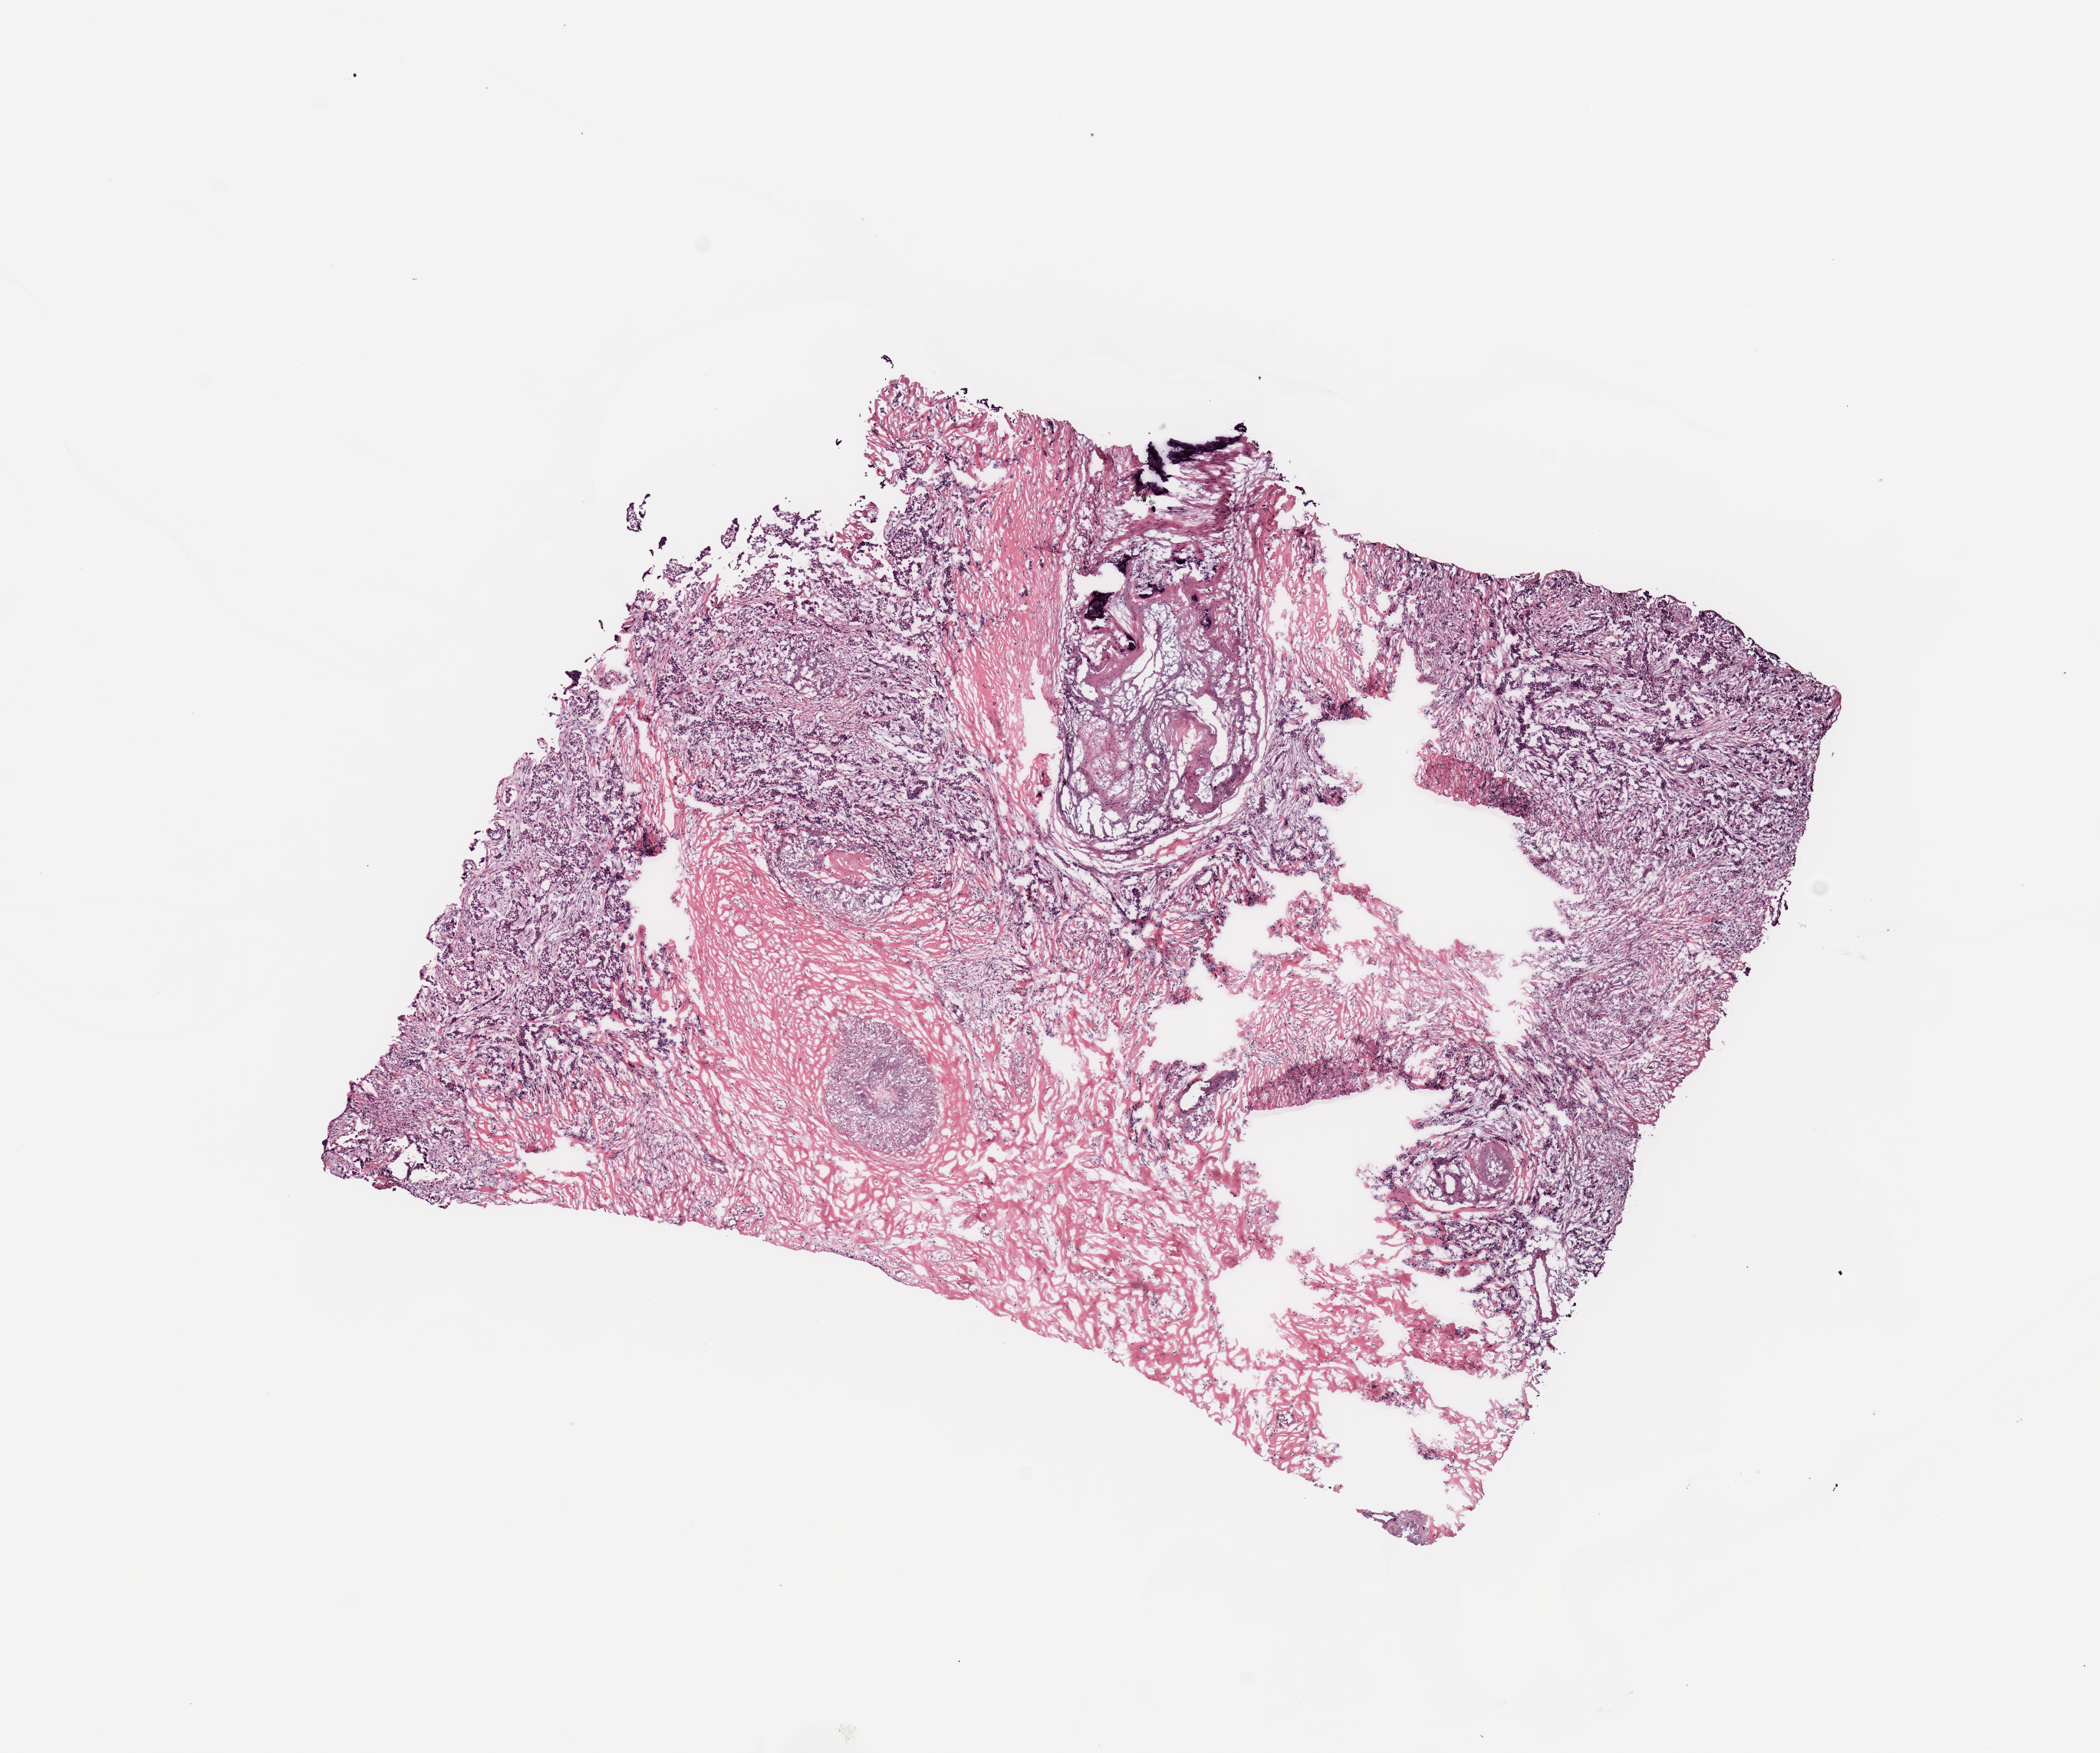
H&E whole-slide image, shown as a low-resolution overview of the whole scanned area (about 10.8 x 9.0 mm, acquisition: 20x scan).
• specimen: breast, tissue type not recorded